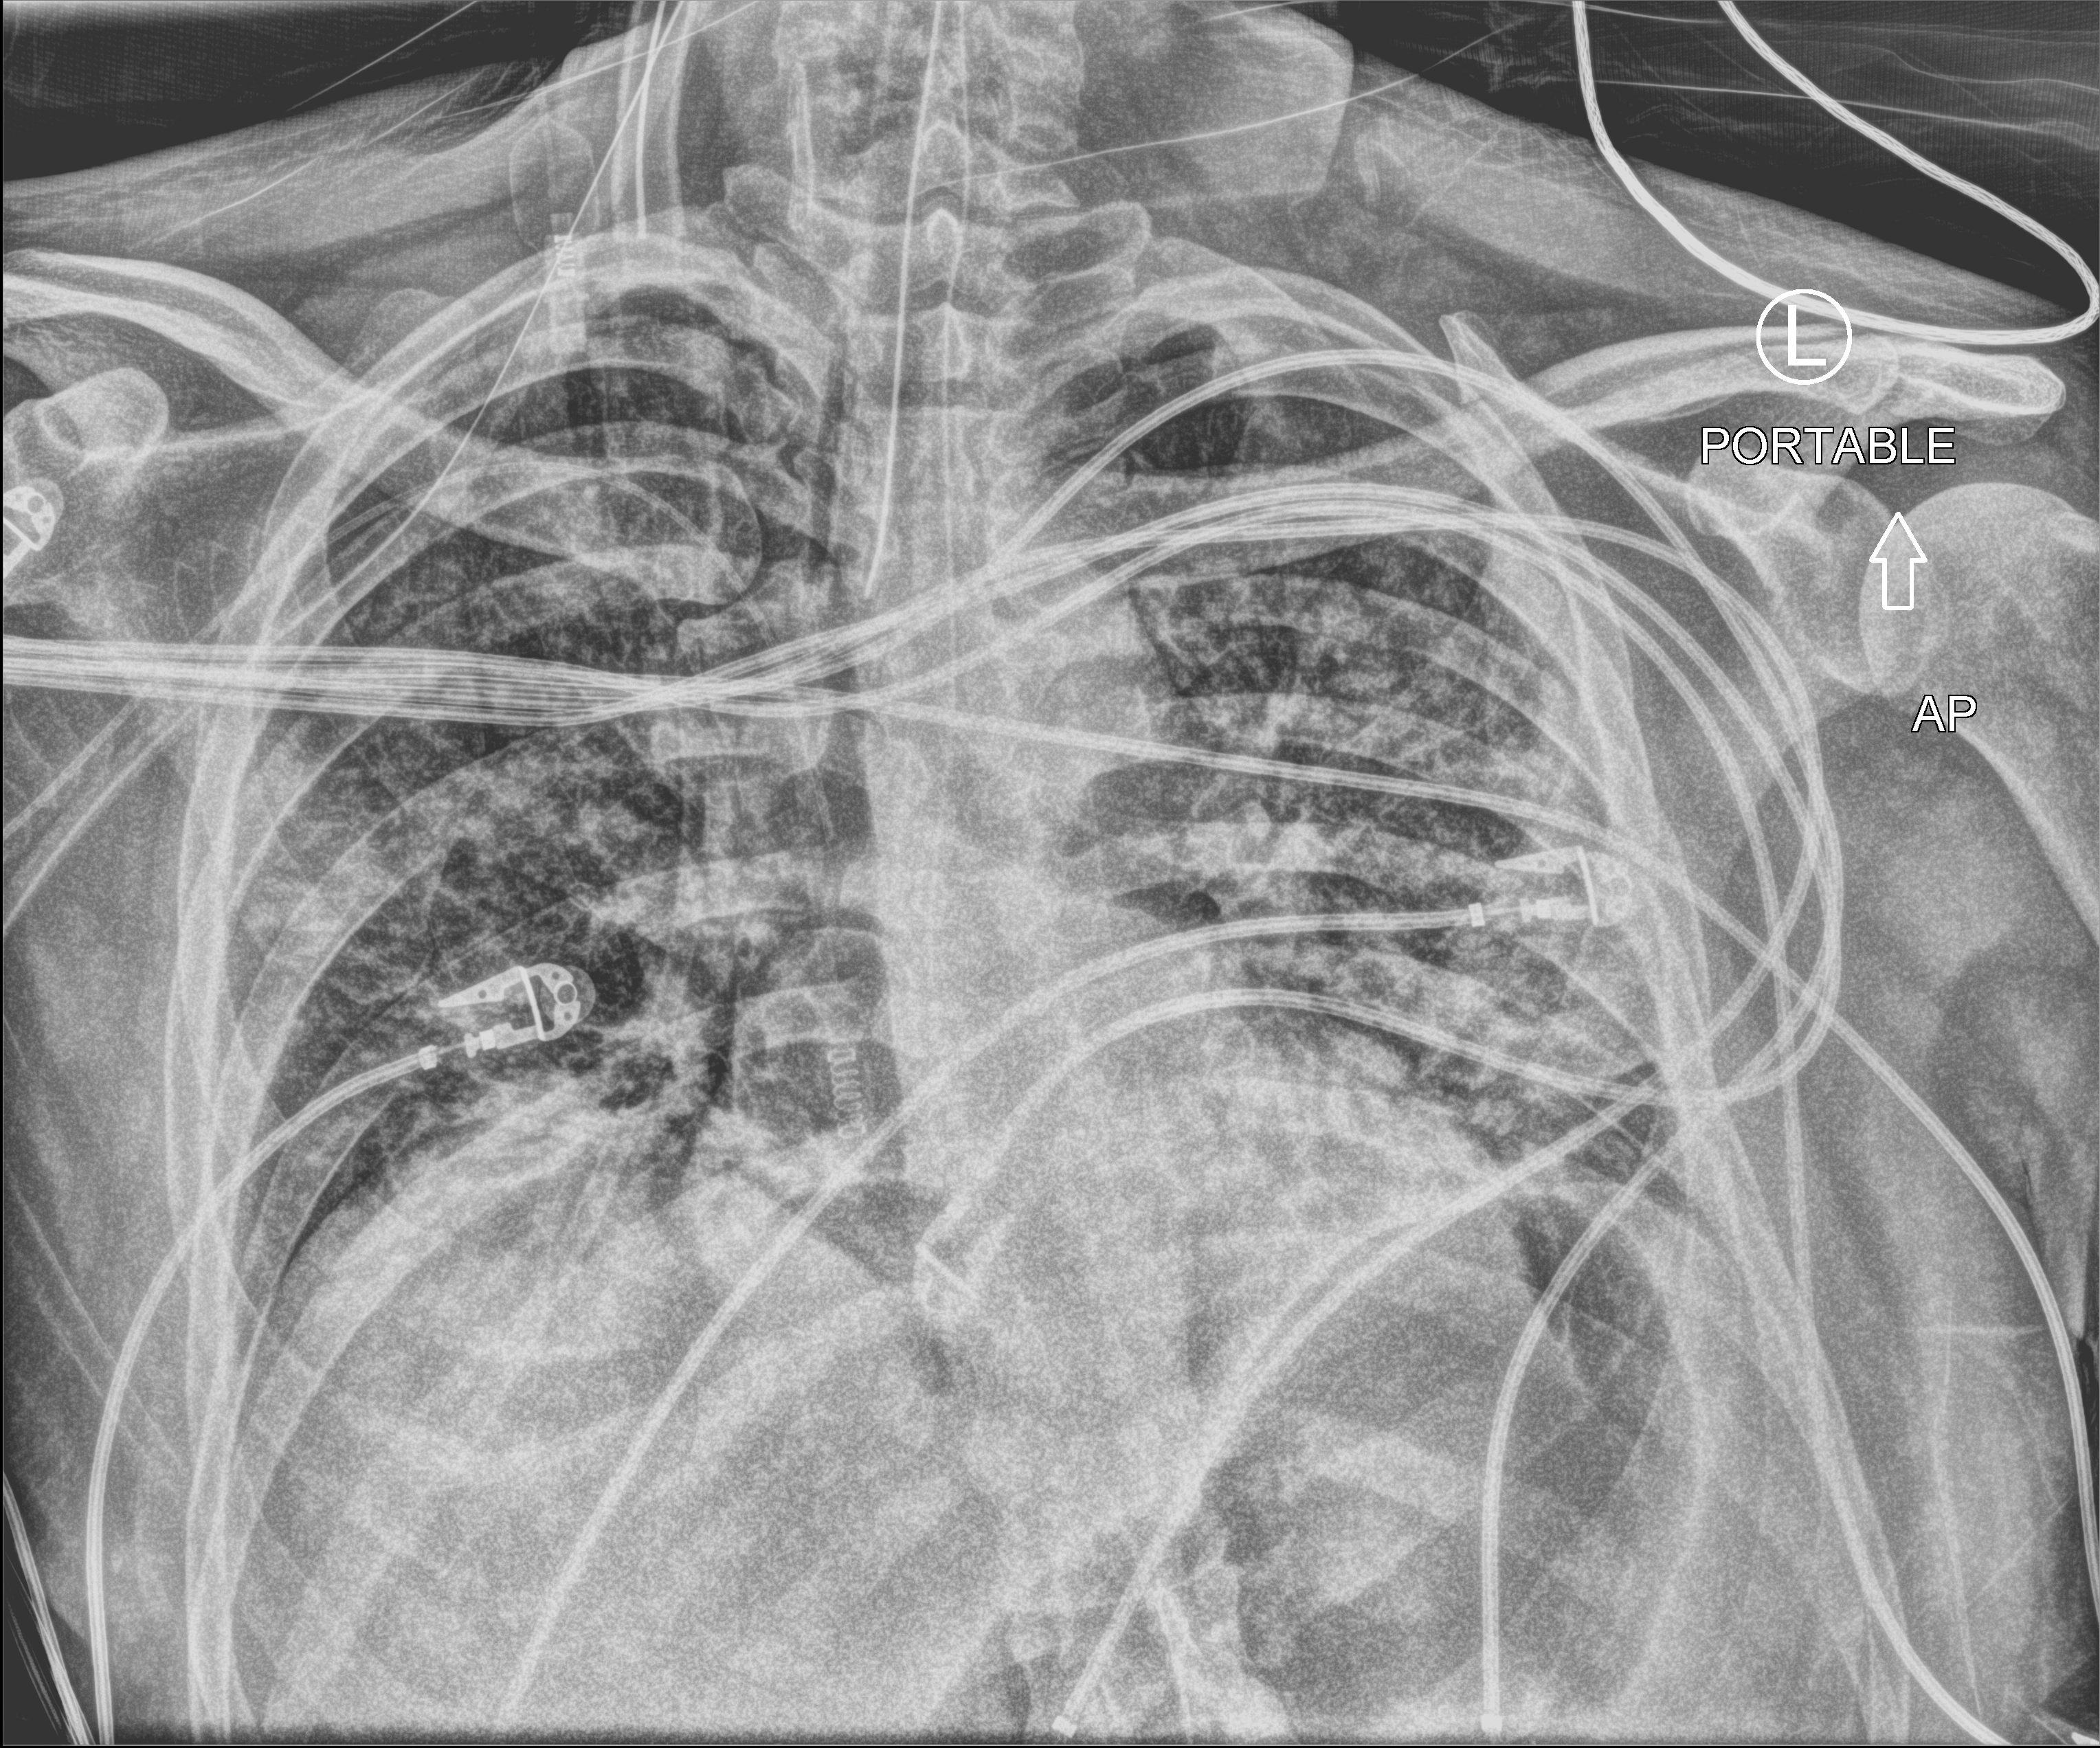
Portable chest radiograph. Male patient hospitalised with COVID-19, age 18–59 years.
From the hospital-stay record, not from the radiograph (when in the stay this image was taken is not recorded):
- admitted to intensive care during this hospital stay: no